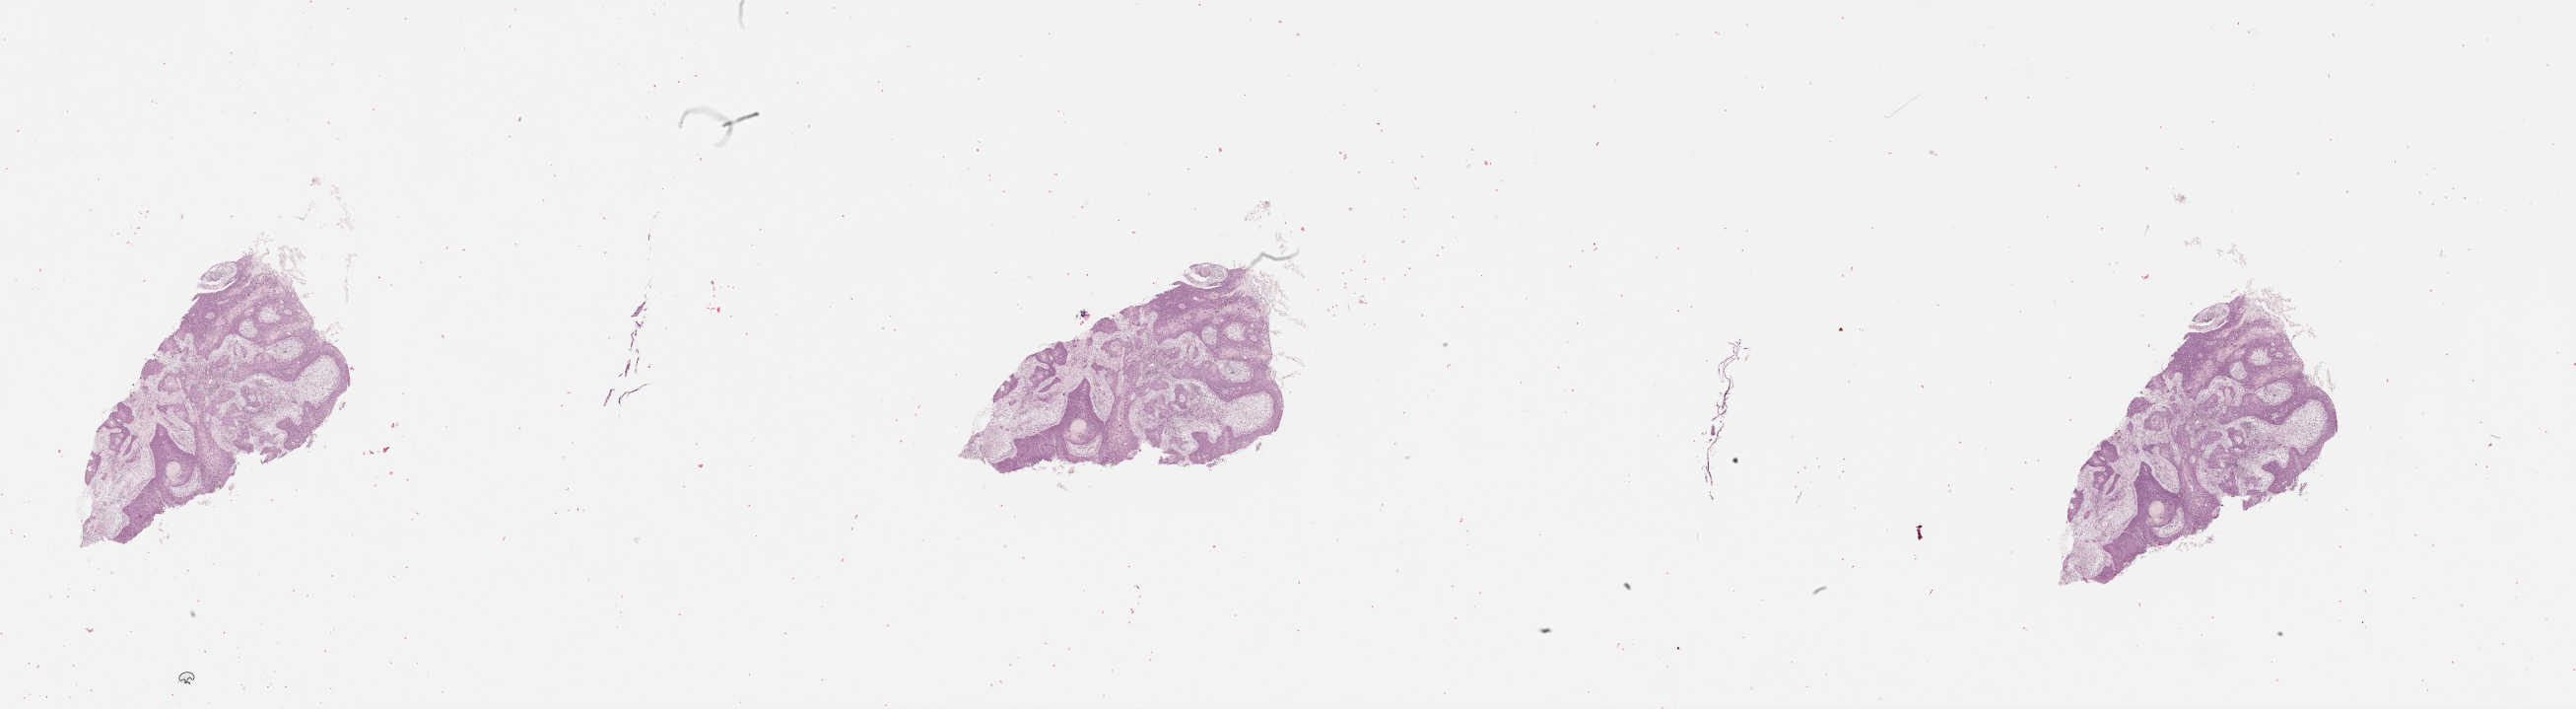
Digitized Hematoxylin and eosin (H&E) stained tissue section (whole slide), whole scanned area (about 42.1 x 11.6 mm, slide scanned at 20x) shown as a low-resolution overview, tumour tissue sample, sampled site: floor of mouth. Male, 64 y/o. Histologic grade: G2 (moderately differentiated). Slide review estimates, as recorded: tumour nuclei 80%, necrosis 5%.
AJCC pathologic stage: IVA. Diagnosis: Squamous cell carcinoma, NOS (floor of mouth, NOS). Primary tumour site (as recorded): oral cavity.